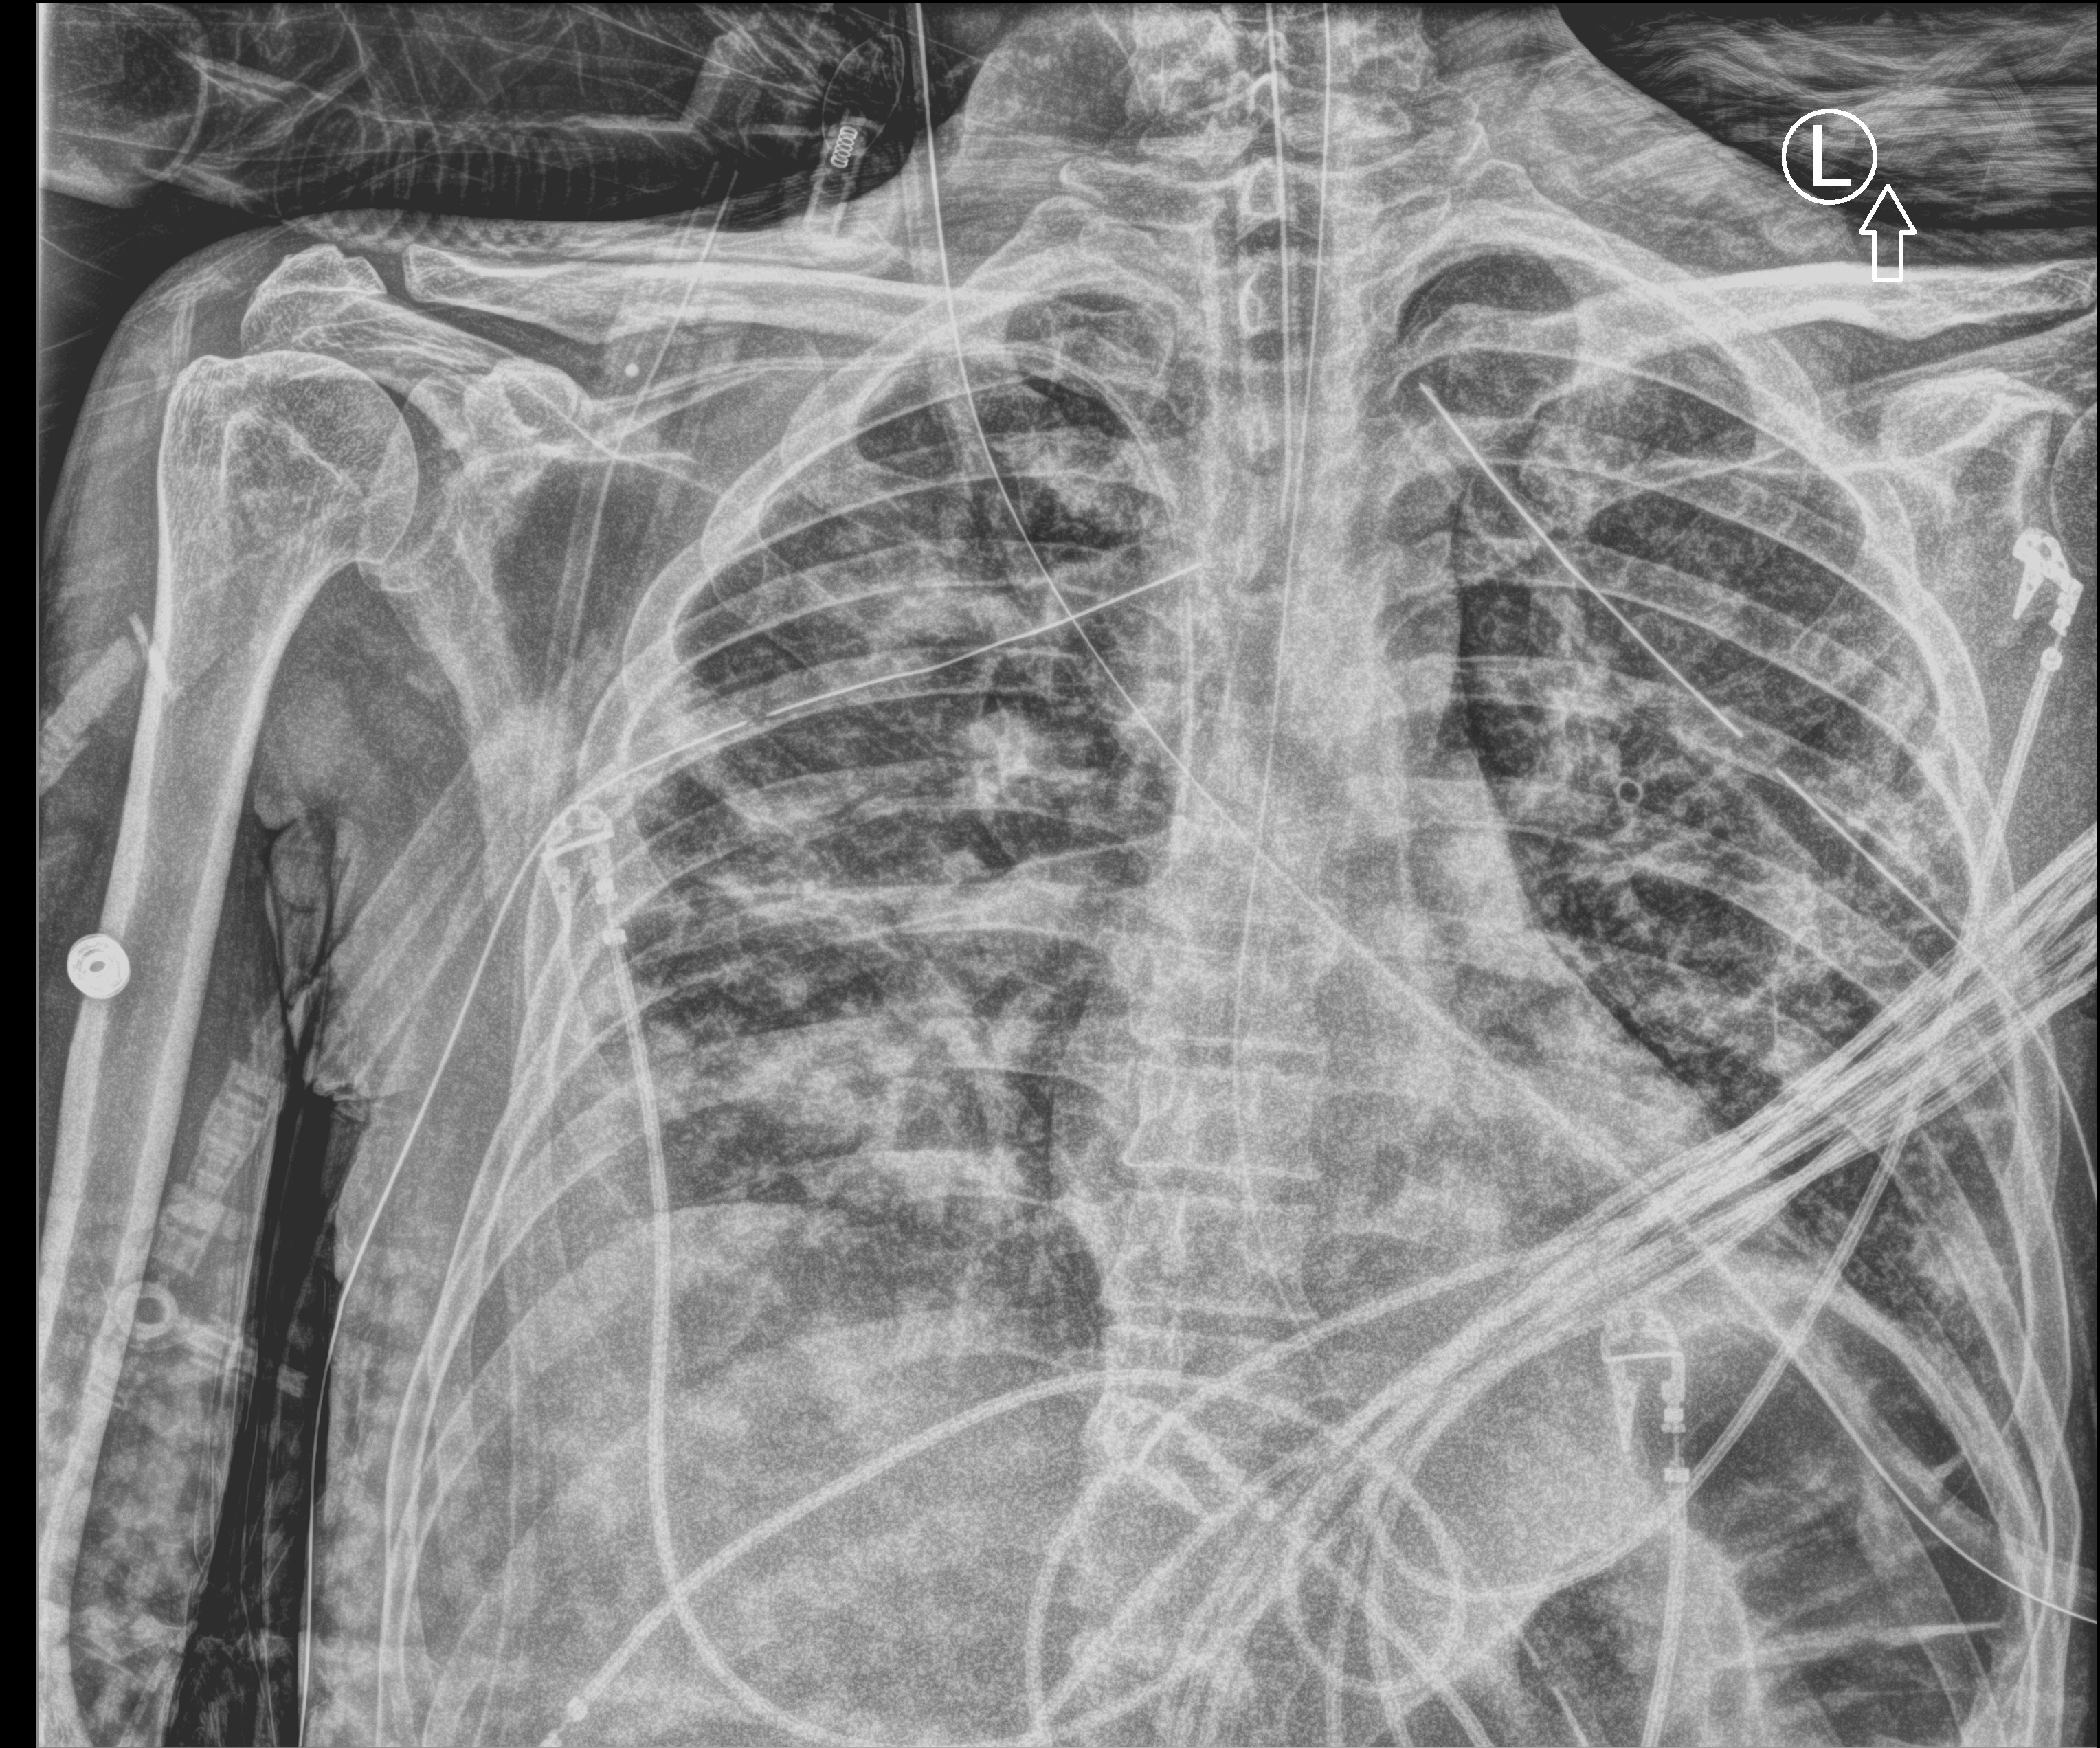
Bedside chest radiograph (computed radiography); anteroposterior (AP) projection. Patient hospitalised with COVID-19; male, aged 18–59 years.
Admission-level facts for this patient (not findings on this image; timing relative to this image not recorded):
- mechanically ventilated during this hospital stay: yes